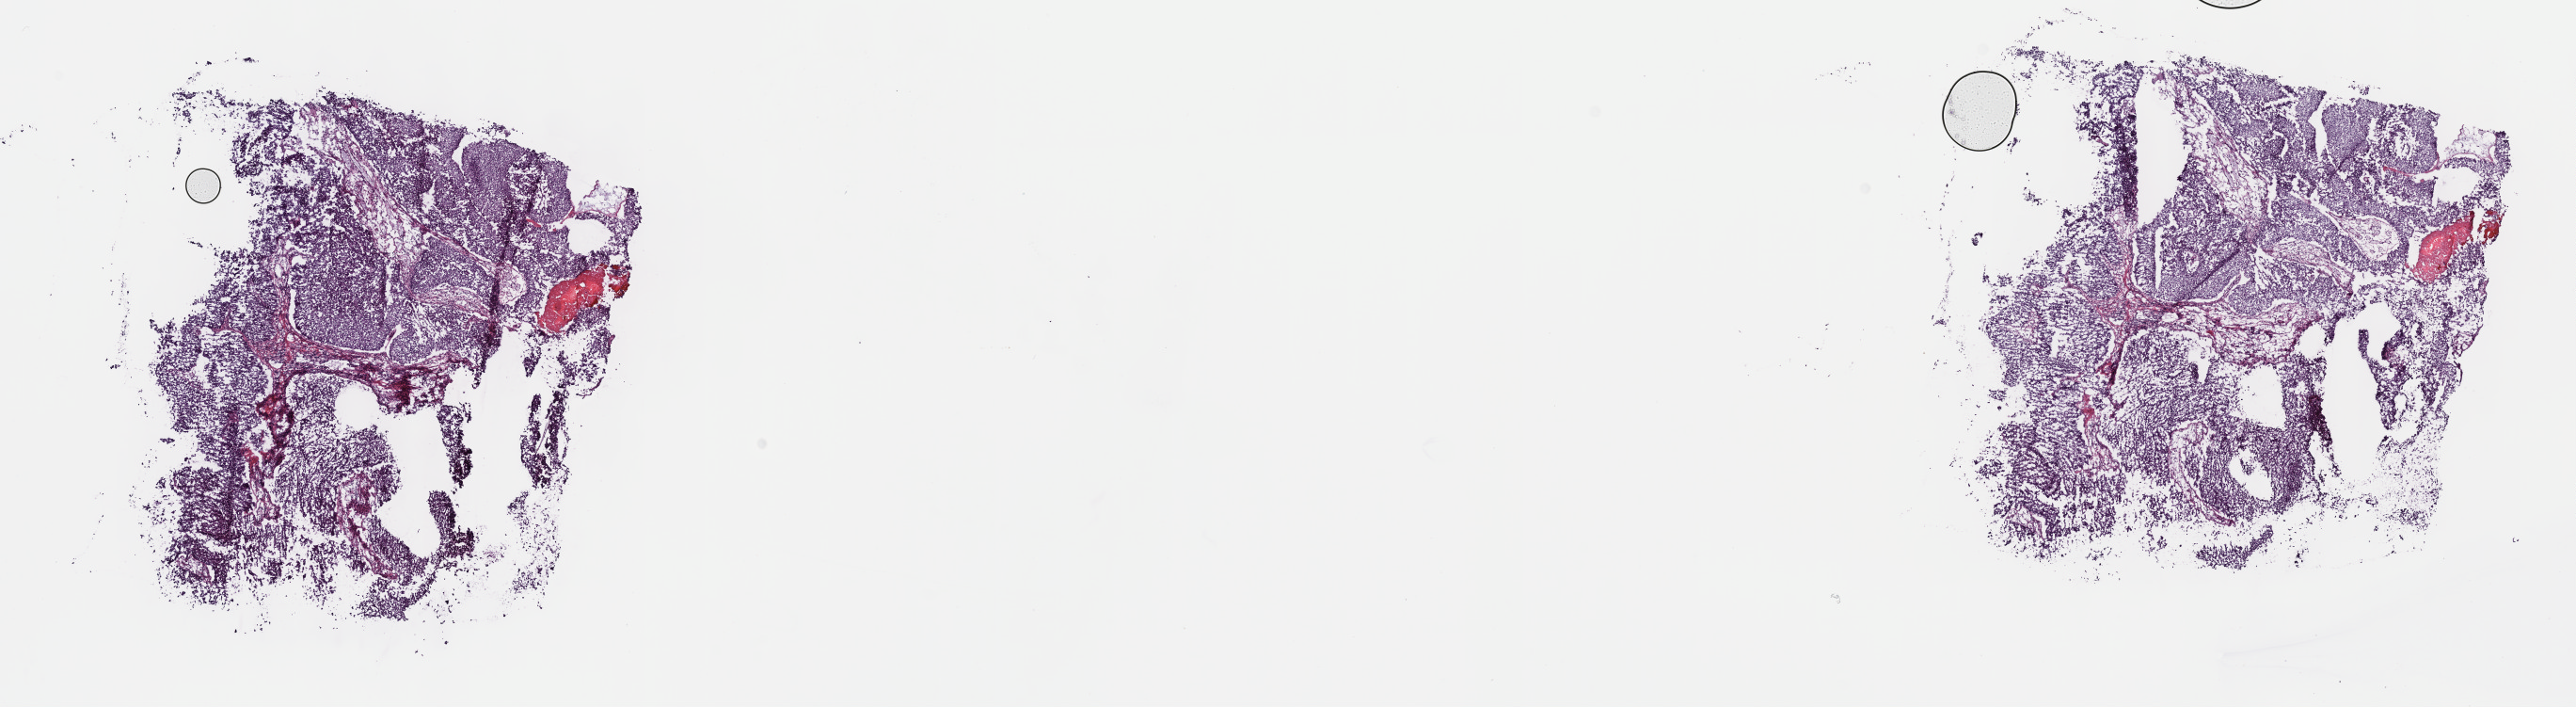
Whole-slide histology image, H&E, low-resolution overview of the scanned area, about 22.1 x 6.1 mm (from a 40x scan), frozen section, sample: primary tumour, bladder. Male, age 52 years at initial diagnosis.
Pathologic diagnosis: Papillary transitional cell carcinoma (lateral wall of bladder).